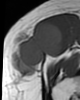
MRI of an extremity soft-tissue mass, one axial slice; MR volume resampled by the dataset authors to the PET/CT grid (not the native acquisition matrix); 3.27 mm slice thickness; 80 × 100 image matrix, field of view 78 × 98 mm. Female patient. Case-level facts recorded for this patient, not image findings: histological type: synovial sarcoma; grade: intermediate; site of the primary tumour: right thigh.
Structures marked on this image (expert contour drawn on MRI and transferred to this co-registered scan by the dataset authors):
- gross tumour volume including surrounding oedema: box from (x=12, y=21) to (x=63, y=77) px
- gross tumour volume (mass): (x=12, y=21)–(x=63, y=77)